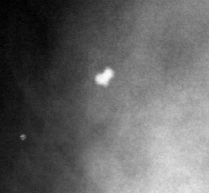
Cropped region of a digitized screen-film mammogram centred on a radiologist-marked abnormality, right breast, MLO view, BI-RADS breast density category 3 (scale 1–4).
- Calcifications, morphology lucent center; BI-RADS assessment category 2; subtlety rating 5 on a 1 (subtle) to 5 (obvious) scale; benign without callback (not worked up further).